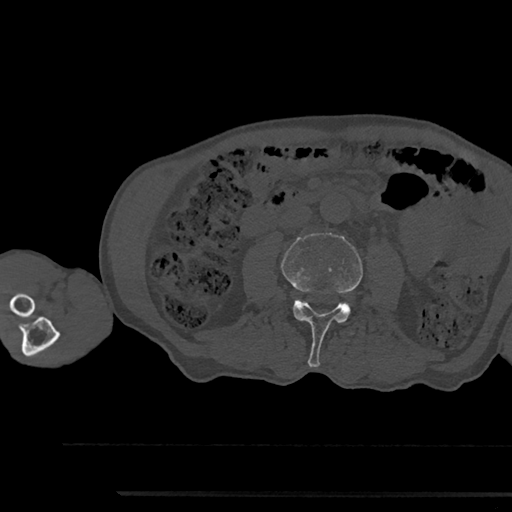
CT including the spine, one axial slice. Reconstruction kernel Br40s/3. Bone window (W 1800 / L 400 HU). 0.5 mm slice thickness. 512 × 512 image matrix. Male patient, age 79 years. Case-level facts recorded for this patient, not image findings: primary cancer: prostate.
Annotated regions visible in this slice (semi-automatically segmented with operator editing):
- L3 vertebra: box from (x=281, y=233) to (x=363, y=367) px